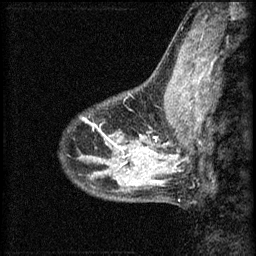
Breast MRI (dynamic contrast-enhanced), one sagittal slice; position 16 of 60 along the scan axis; 3 images stored at this slice position (order not interpretable as contrast timing); 1.5 T; TE 4.2 ms, TR 8.2 ms; 2 mm slice thickness; 256 × 256 image matrix. Patient: female, 40 years.
Annotated regions visible in this slice (semi-automatically segmented with operator editing):
- analysis volume of interest (the breast-tissue region the enhancement analysis was run in; not a lesion): bounding box <108,108,167,159> (left, top, right, bottom; pixels)
- tumour enhancement mask (voxels above the 70 % enhancement threshold inside the analysis volume of interest): <114,140,157,159>